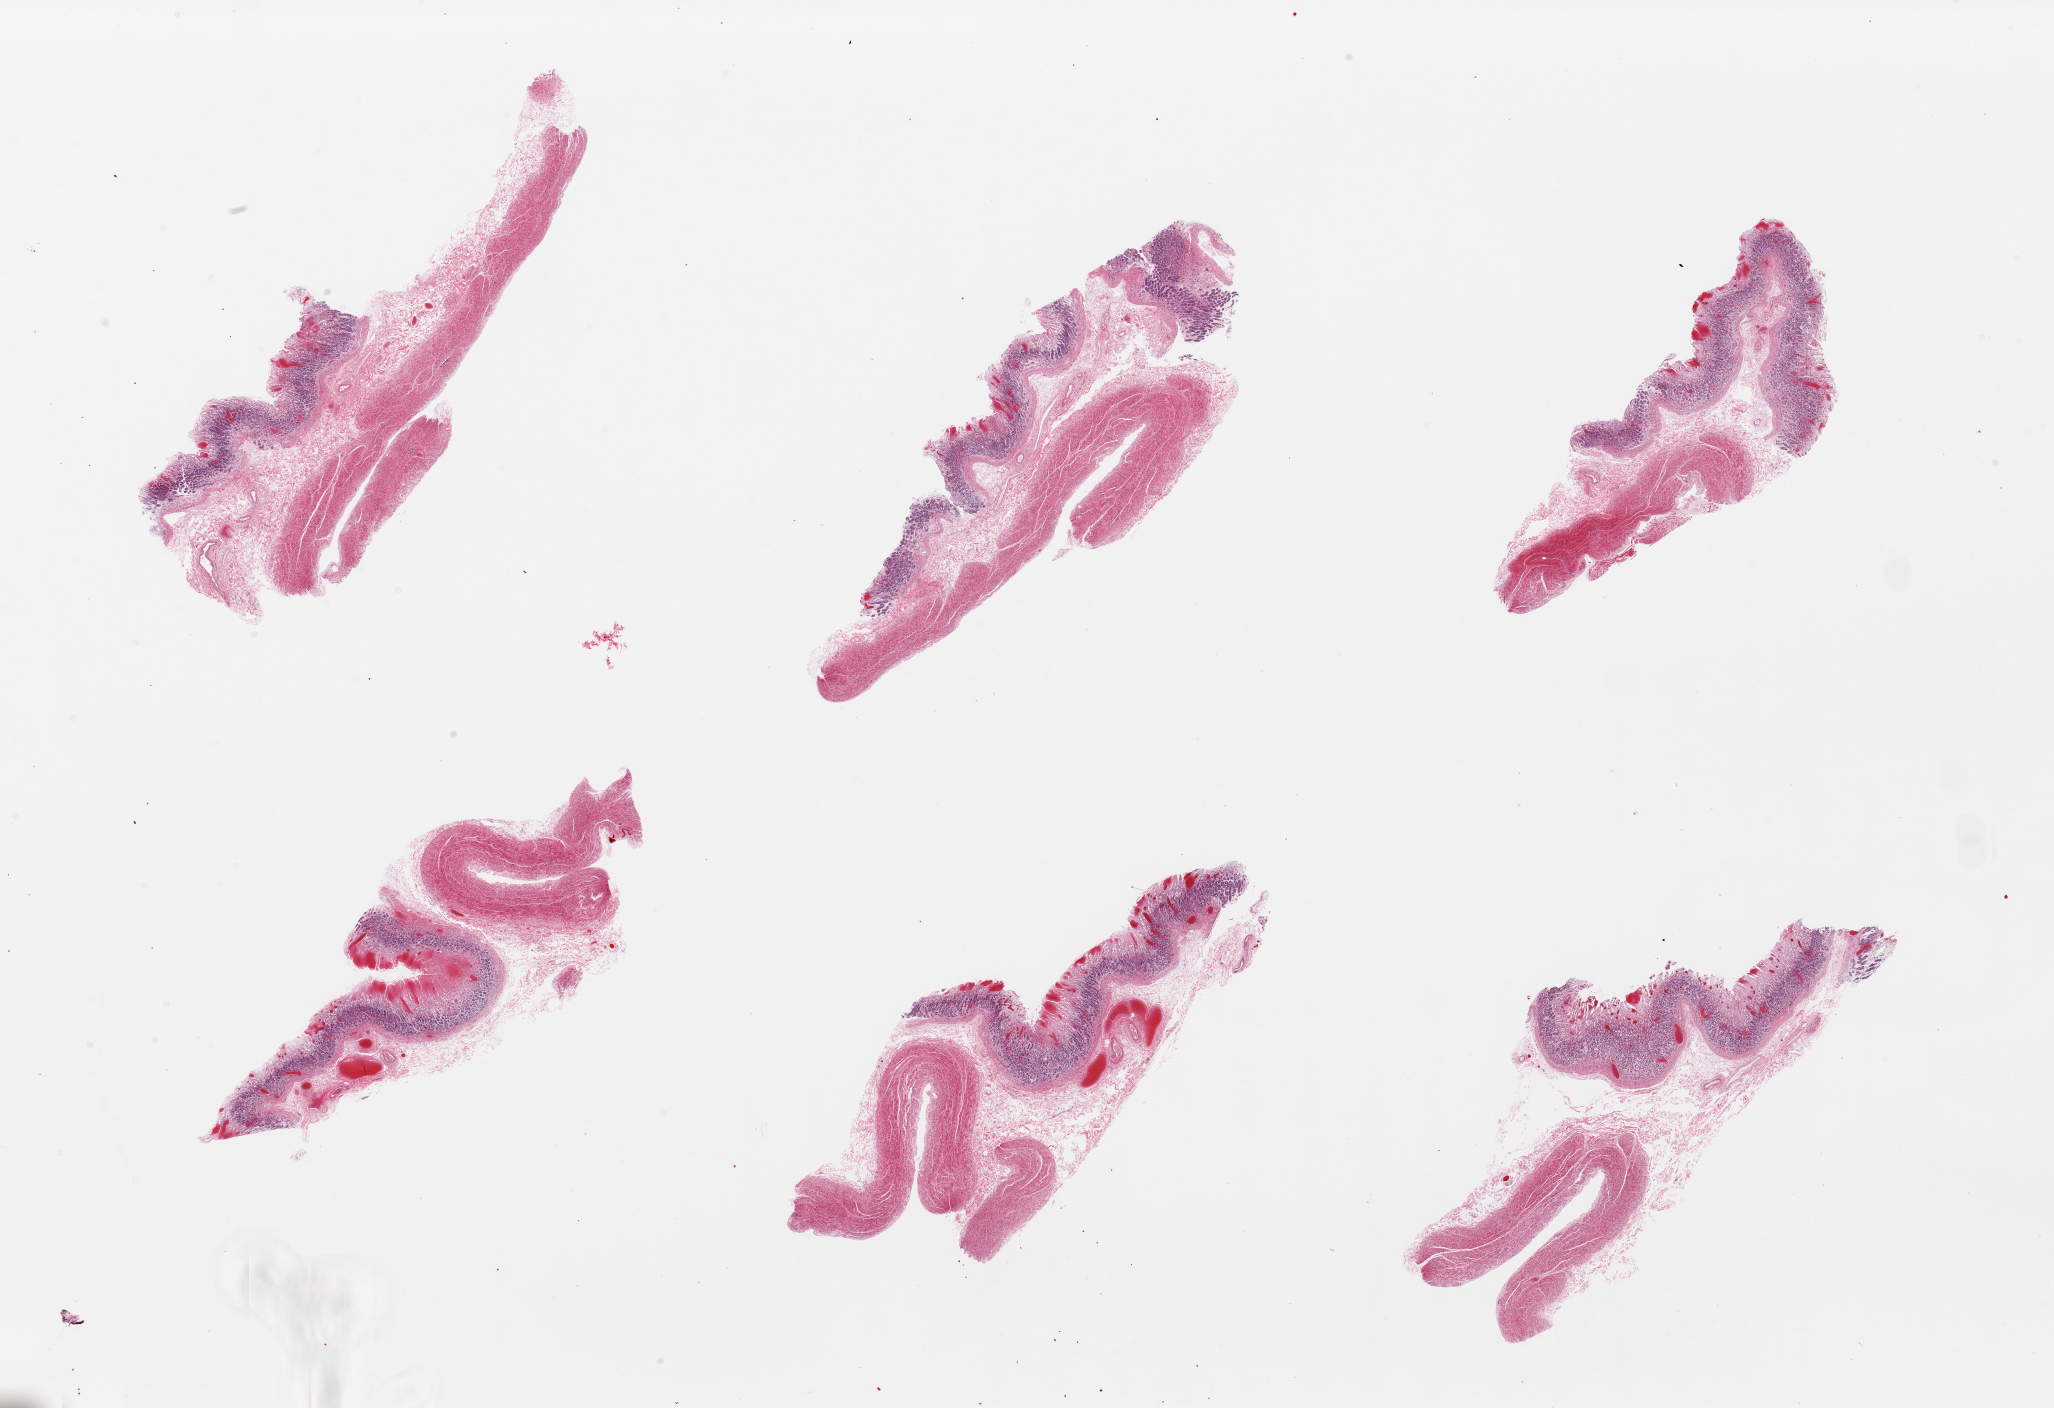
Whole-slide image, hematoxylin and eosin (H&E) stain, whole scanned area (about 32.5 x 22.3 mm) shown as a low-resolution overview; PAXgene-fixed paraffin-embedded (PFPE) section; sampled site (target tissue): stomach; donor tissue sample. Female donor.
• pathologist's review note for this sample: 6 pieces; mucosa up to ~1mm thick but badly autolyzed and/or sloughing